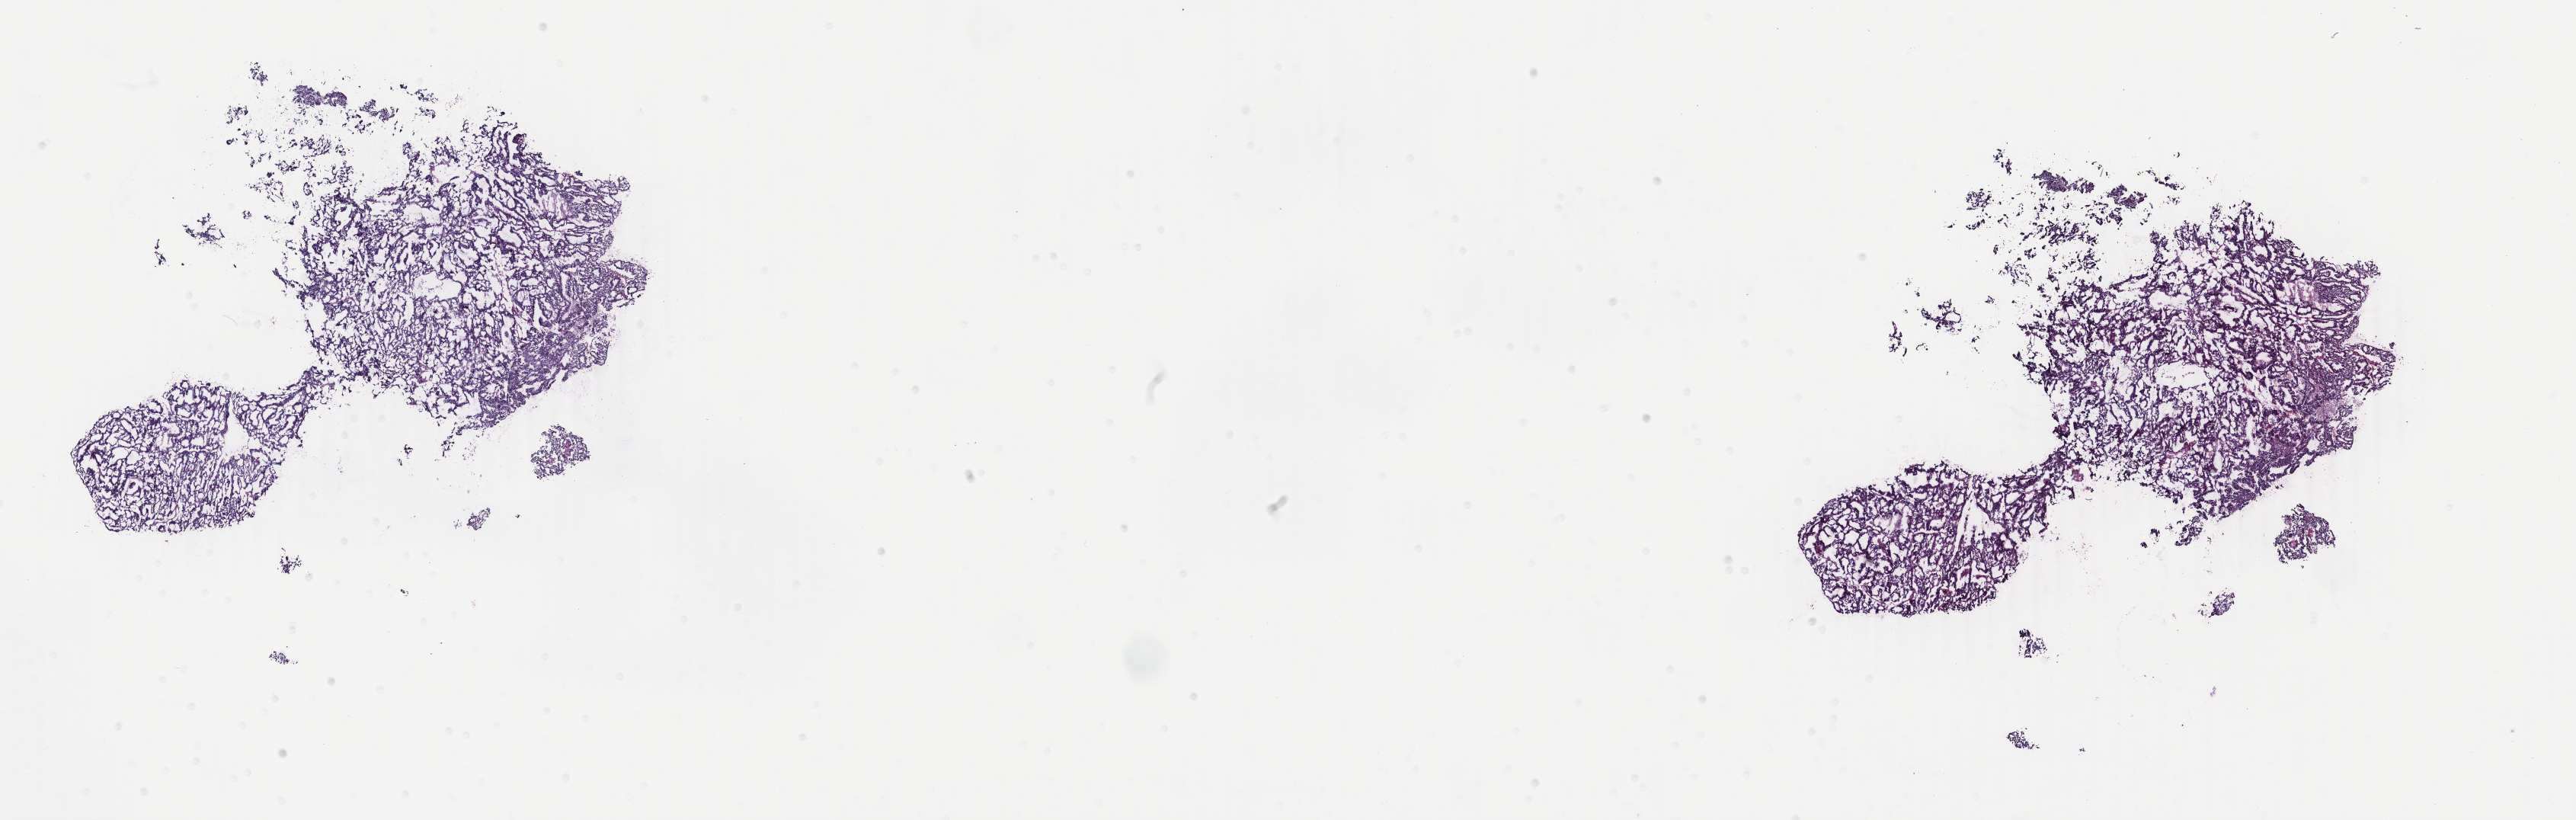
H&E-stained whole-slide image, shown as a low-resolution overview of the whole scanned area (about 26.9 x 8.6 mm), frozen section from the bottom of the tissue portion, sample: primary tumour, uterus. Female, age 67 years at initial diagnosis. Histologic grade: G1 (well differentiated). Pathologist review of this section (percent, as recorded): tumour cells 92%, tumour nuclei 98%, normal cells 0%, stromal cells 3%, necrosis 5%. Inflammatory infiltration, as recorded: lymphocyte infiltration 0%, monocyte infiltration 0%, neutrophil infiltration 0%.
* FIGO stage: IA
* diagnosis: Endometrioid adenocarcinoma, NOS (endometrium)